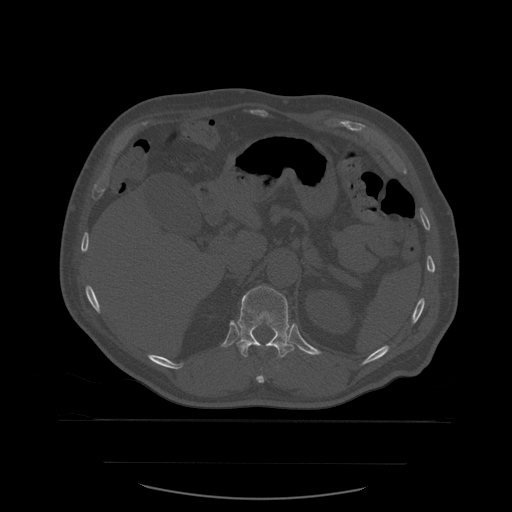
CT including the spine, one axial slice. Position 276 of 590 along the scan axis. Bone window (W 1800 / L 400 HU). 1.25 mm slice thickness. 512 × 512 image matrix, field of view 479 × 479 mm. Patient age 71 years. Case-level facts recorded for this patient, not image findings: primary cancer: lung; vertebrae with lytic lesions (as recorded): T1, T2, L5, S1.
Outlined on this slice (semi-automatically segmented with operator editing):
- T11 vertebra: box from (x=256, y=375) to (x=265, y=383) px
- T12 vertebra: (x=236, y=286)–(x=295, y=358)